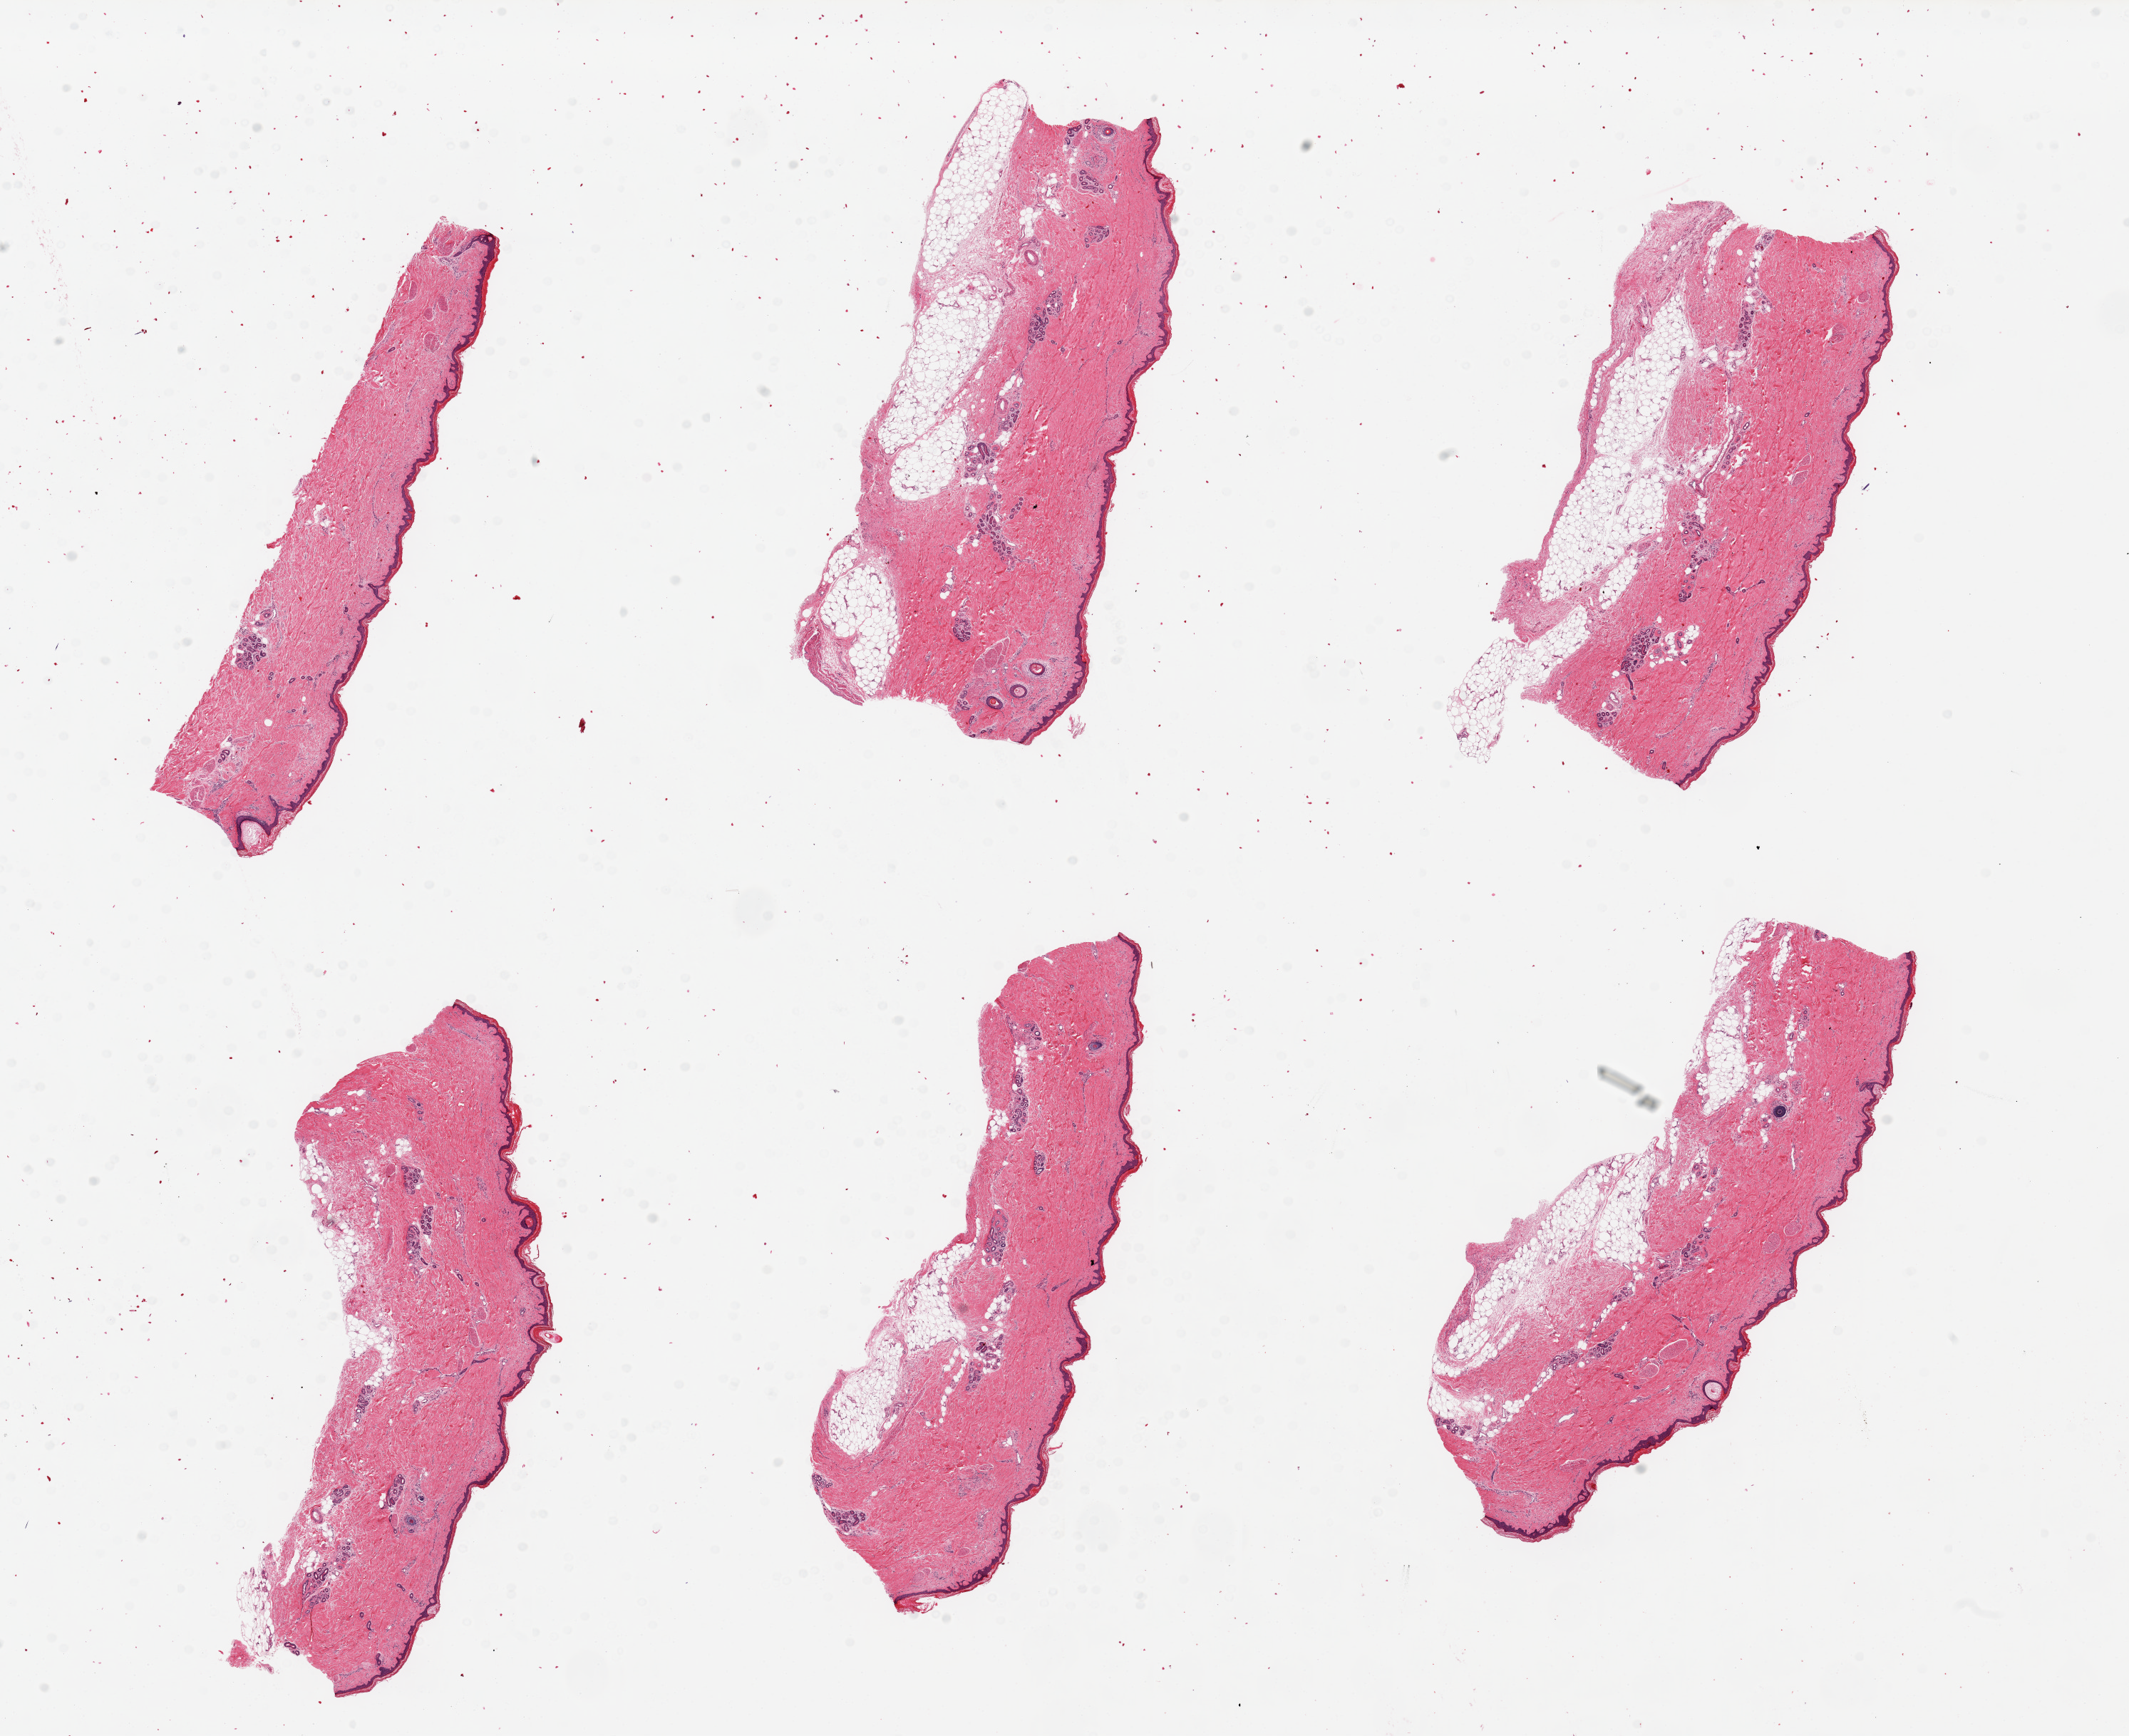
Haematoxylin and eosin whole-slide image, a low-resolution overview of the entire scanned area, about 23.6 x 19.3 mm. PAXgene-fixed paraffin-embedded (PFPE) section. Sampled site (target tissue): skin of lower leg. Donor tissue sample. Male donor.
* pathologist's review note for this sample: 6 pieces, up to 8x3mm; 3 have up to 1 mm subcutaneous adipose